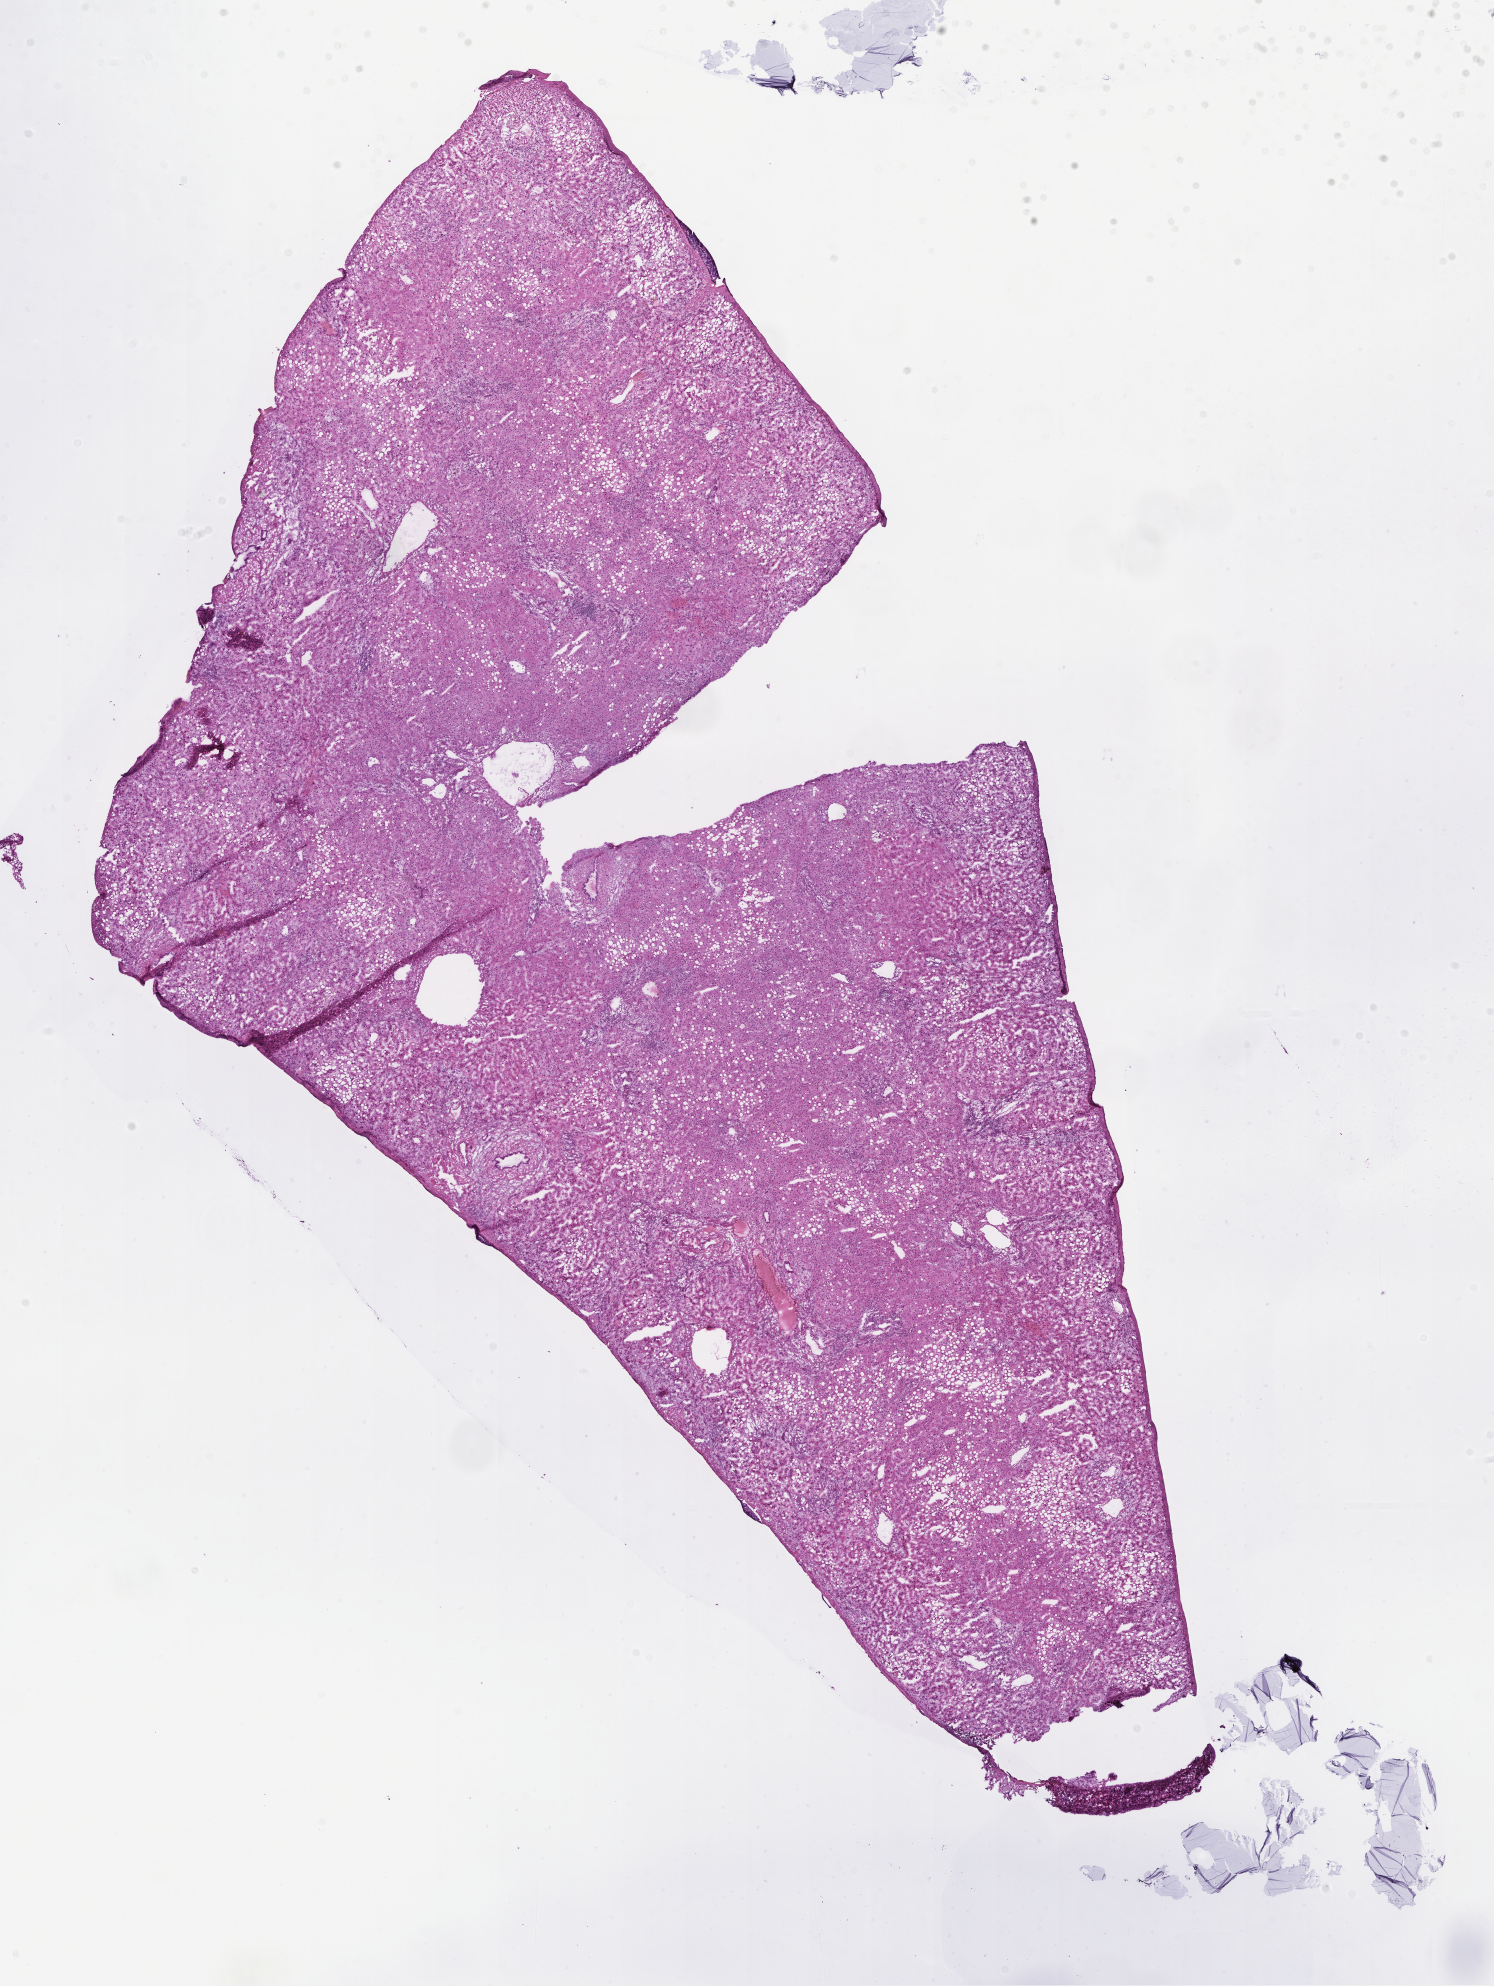
Whole-slide image, haematoxylin and eosin stain, low-resolution overview of the scanned area, about 12.1 x 16.1 mm, cryosection, specimen: normal-tissue sample (non-tumor) from a patient with adenocarcinoma, NOS, site: colon. Male patient; age at initial diagnosis 70 years. Slide review estimates, as recorded: tumor cells 0%, tumor nuclei 0%, stromal cells 0%, necrosis 0%, normal cells 100%. Infiltration values recorded for this section: lymphocyte infiltration 5%, monocyte infiltration 2%, neutrophil infiltration 0%.
This section: non-tumor tissue sample; the patient's diagnosis is given above. Section: bottom of the tissue portion.